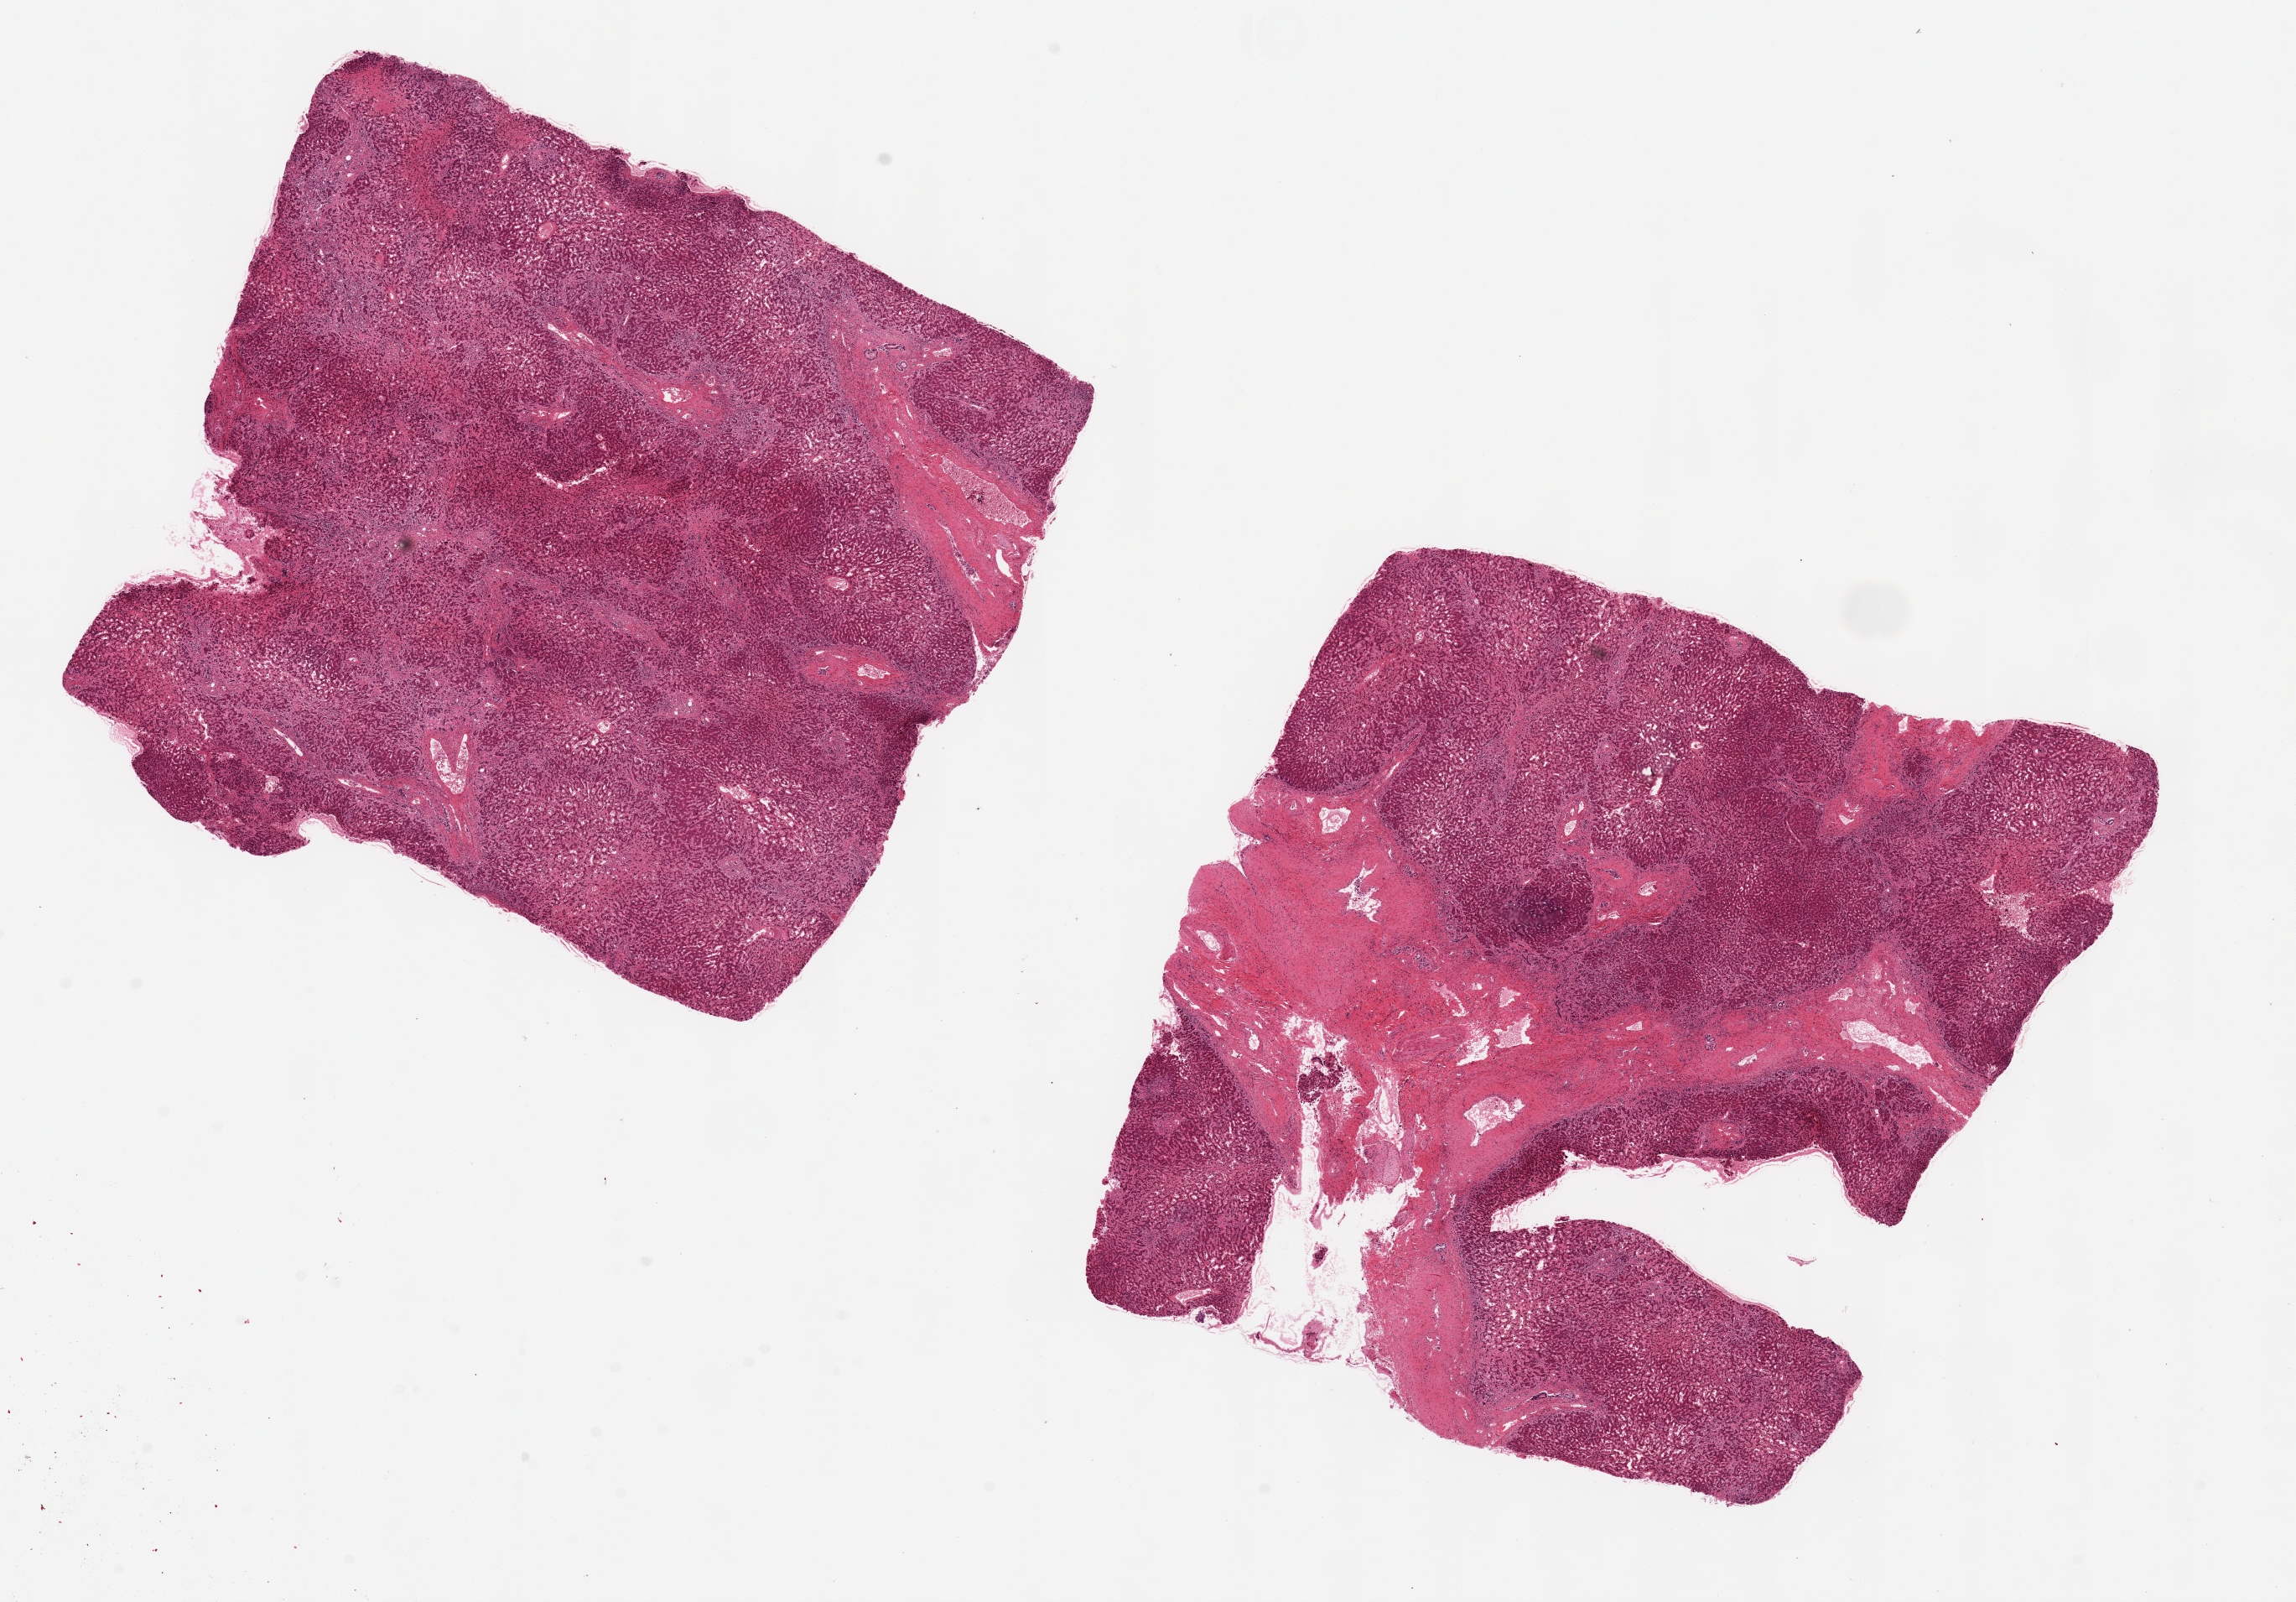
H&E whole-slide image — a low-resolution overview of the entire scanned area, about 21.7 x 15.1 mm (acquisition: 20x scan), PAXgene-fixed paraffin-embedded (PFPE) section, target tissue: liver, donor tissue sample.
- reviewer comment on this tissue sample: 2 ~ 8x8mm aliquots, ? fibrosis; request Masson